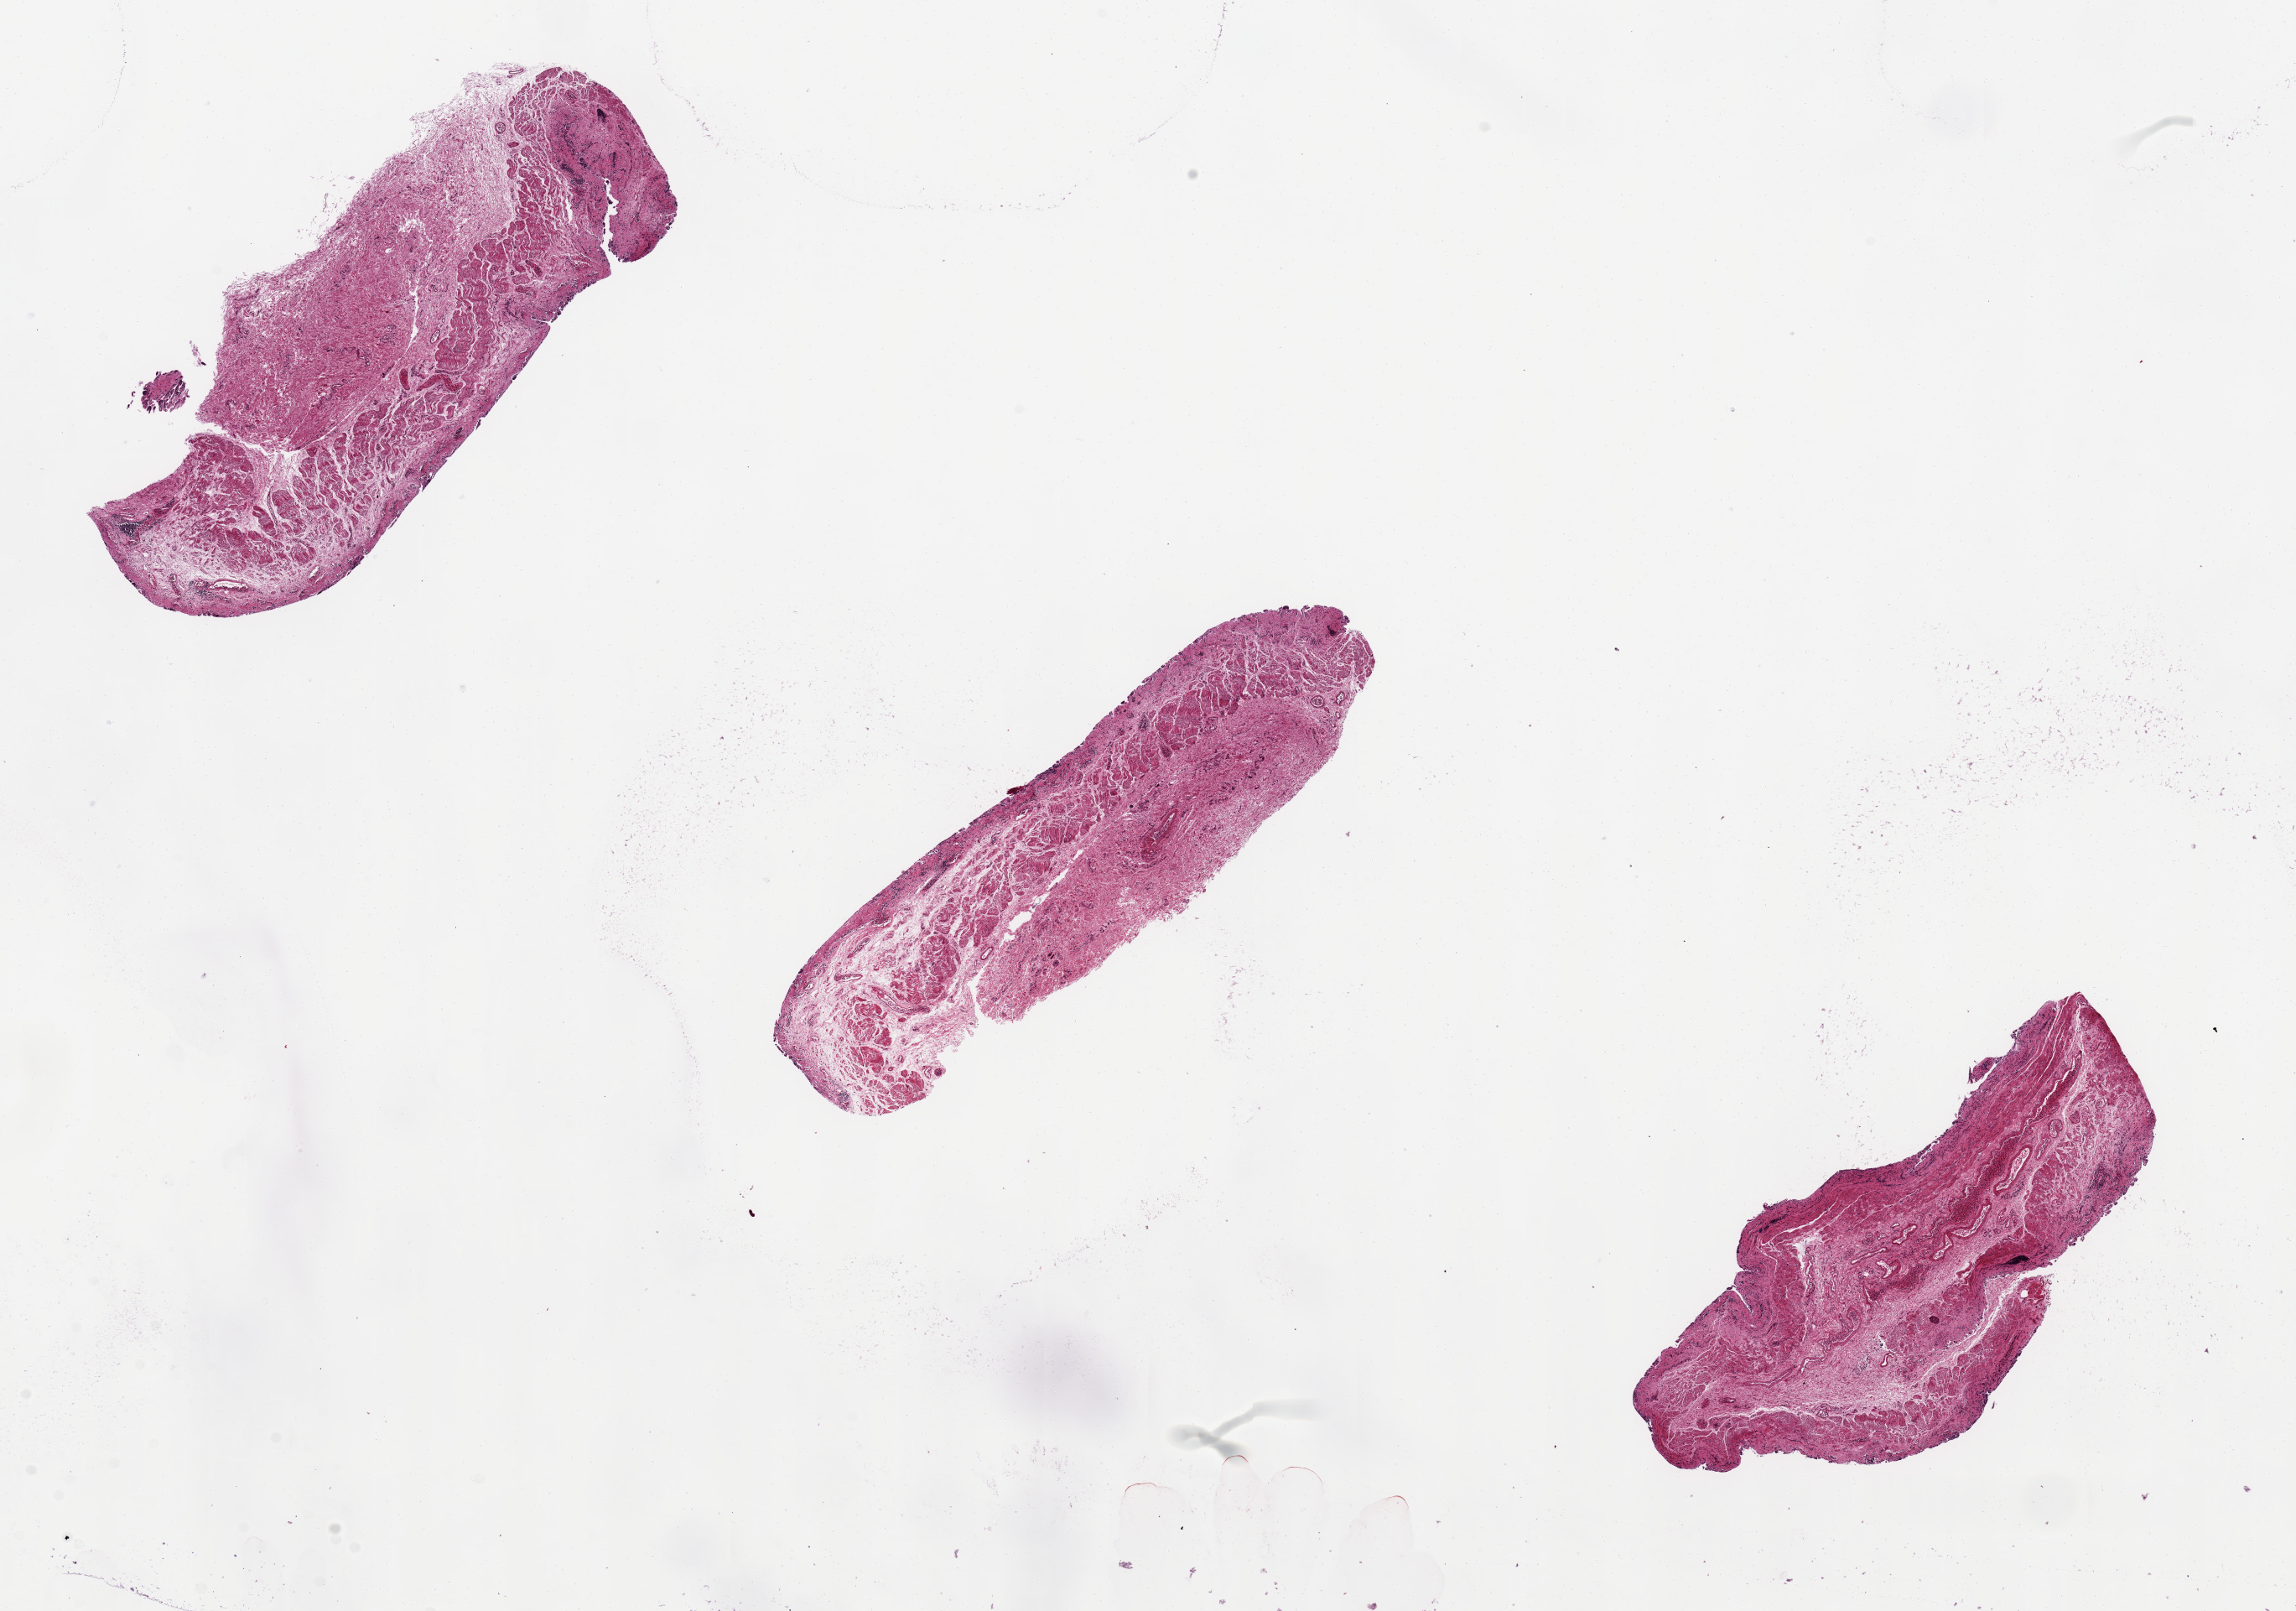
Digitized H&E-stained section — a low-resolution overview of the entire scanned area, about 21.7 x 15.2 mm; PAXgene-fixed, paraffin-embedded tissue; section of esophageal mucous membrane (target tissue); tissue donor sample. Male donor.
Pathologist's review note for this sample: 3 `6x2.5mm pieces. Mucosa near totally sloughed, a few foci look glandular. ? location-GE junction?.